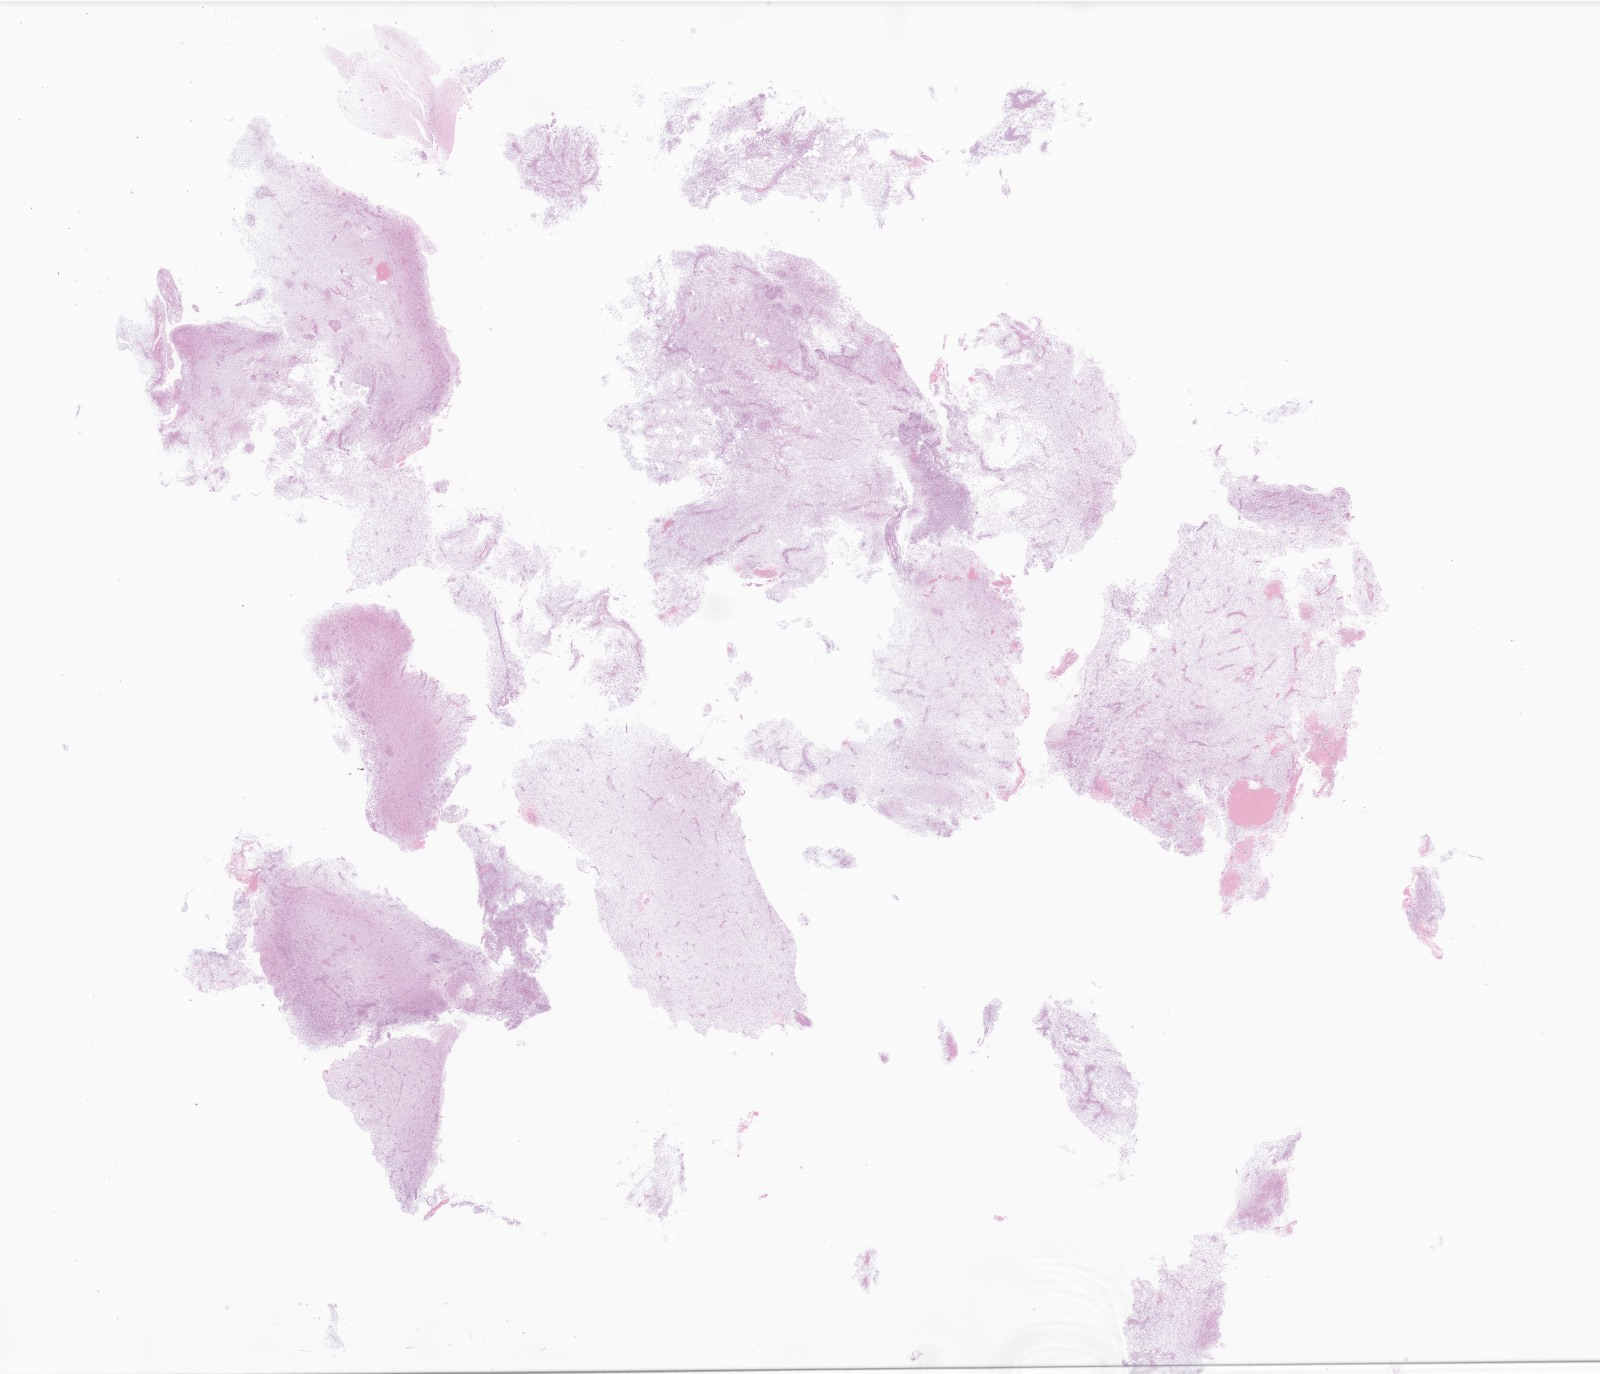
Whole-slide image, haematoxylin and eosin stain of tumor tissue from the brain, whole scanned area (about 27.0 x 23.2 mm) shown as a low-resolution overview; formalin-fixed paraffin-embedded section. Patient female; age 37 months (3 years 1 month).
Diagnosis (ICD-O-3 morphology term): Pilocytic astrocytoma.